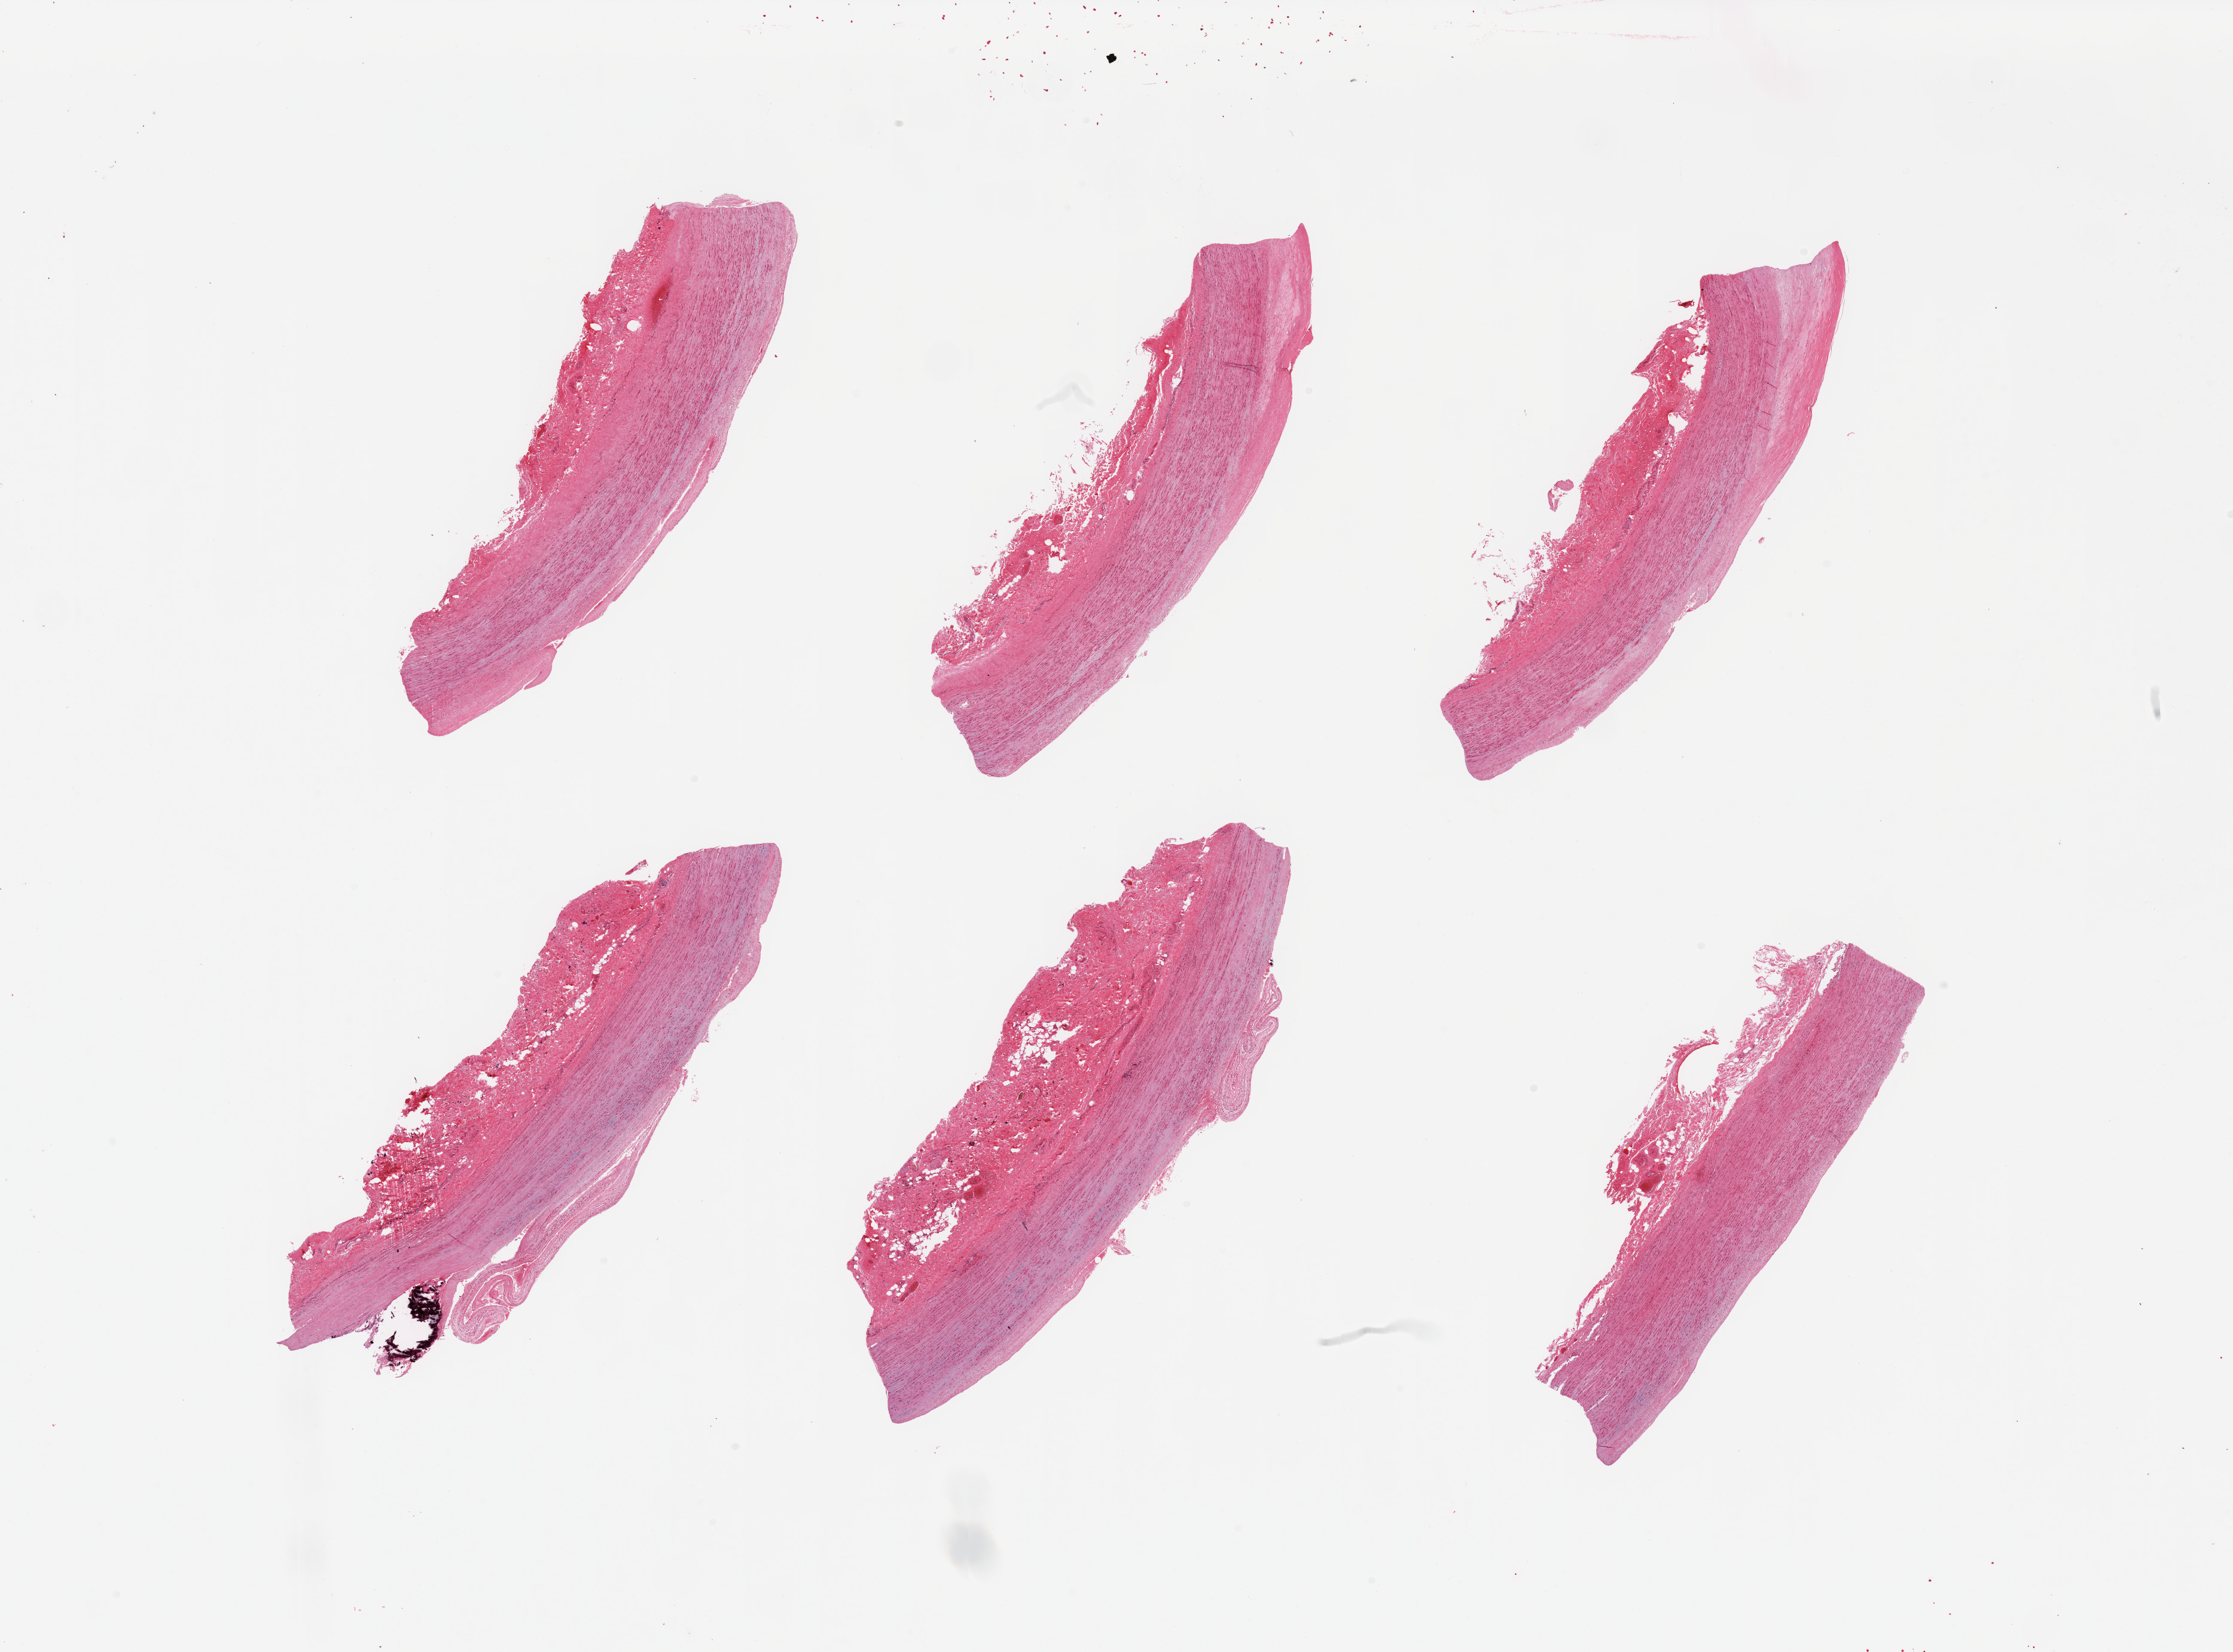
Digitized H&E-stained section, low-resolution overview of the scanned area, about 29.5 x 21.9 mm (acquisition: 20x scan). PAXgene-fixed, paraffin-embedded tissue. Target tissue: aorta. Tissue donor sample. Male donor.
- review note (as recorded): 6 pieces; atherosclerotic plaques up to 0.8mm thick; adventitia up to 1.5mm thick; media appears moderately degenerated